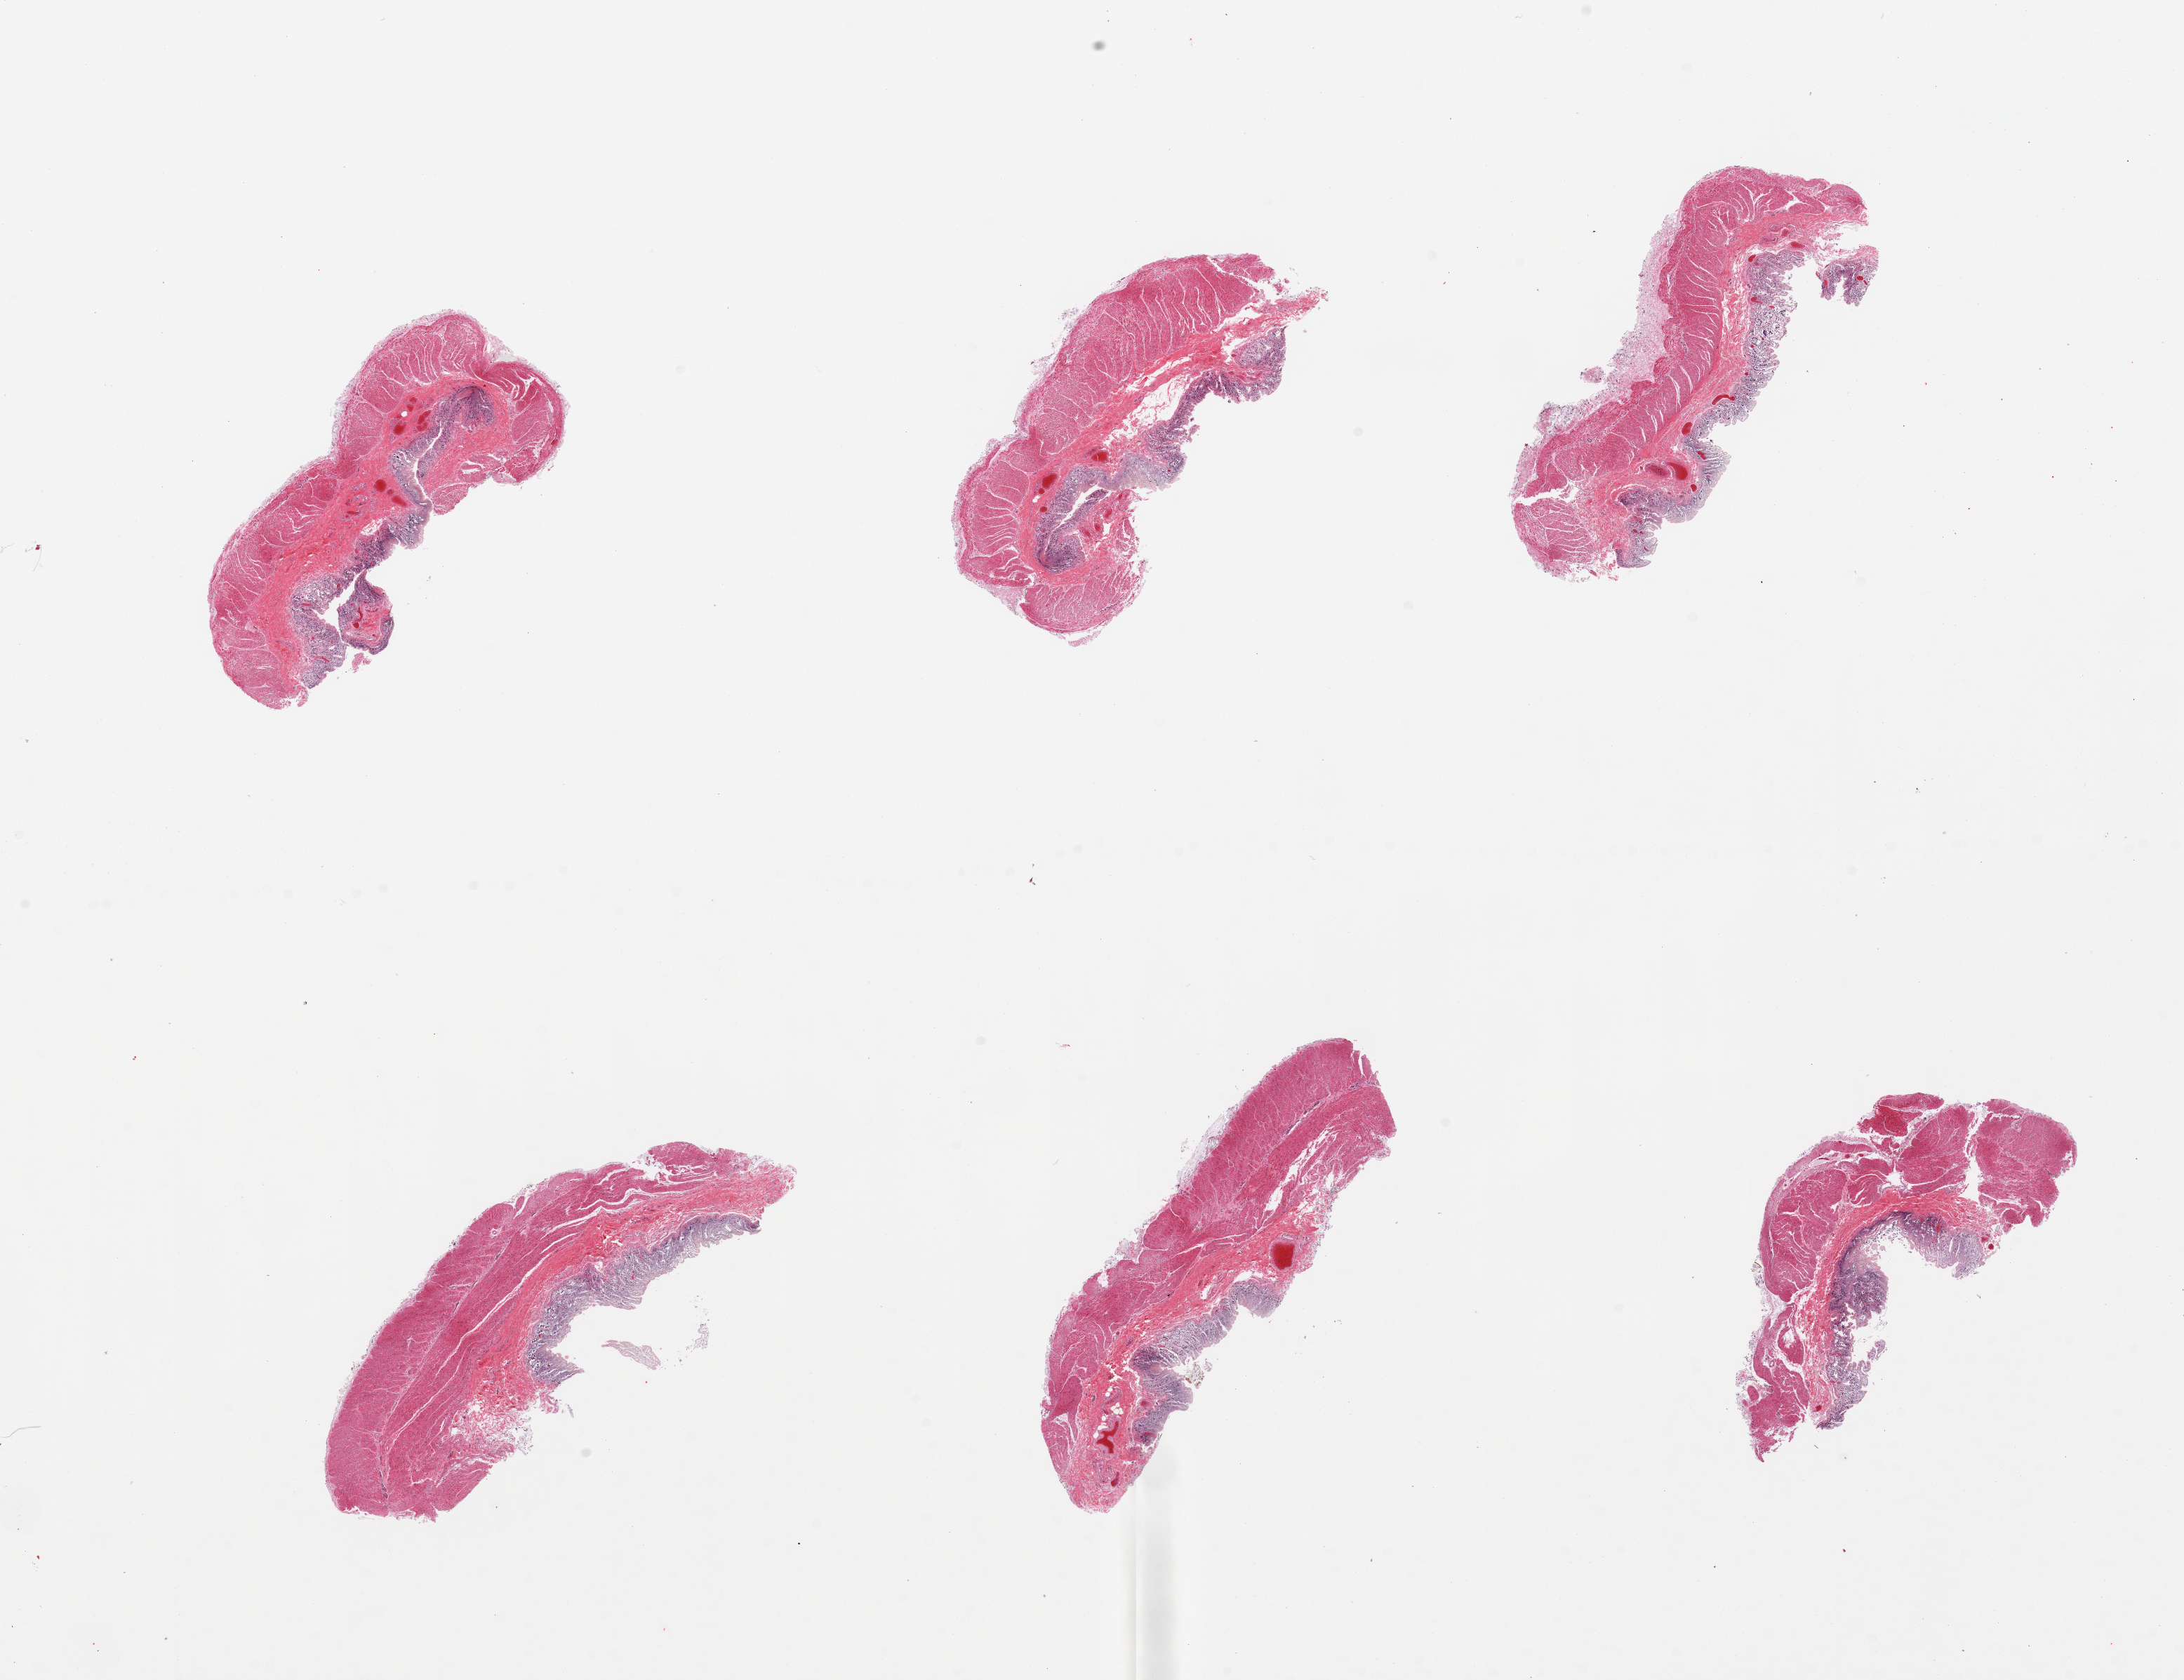
Whole-slide image, H&E stain, shown as a low-resolution overview of the whole scanned area (about 24.6 x 18.9 mm, from a 20x scan). PAXgene-fixed, paraffin-embedded tissue. Section of transverse colon (target tissue). Donor tissue sample. Donor: female.
- review note (as recorded): 6 pieces, mucosa totally autolyzed